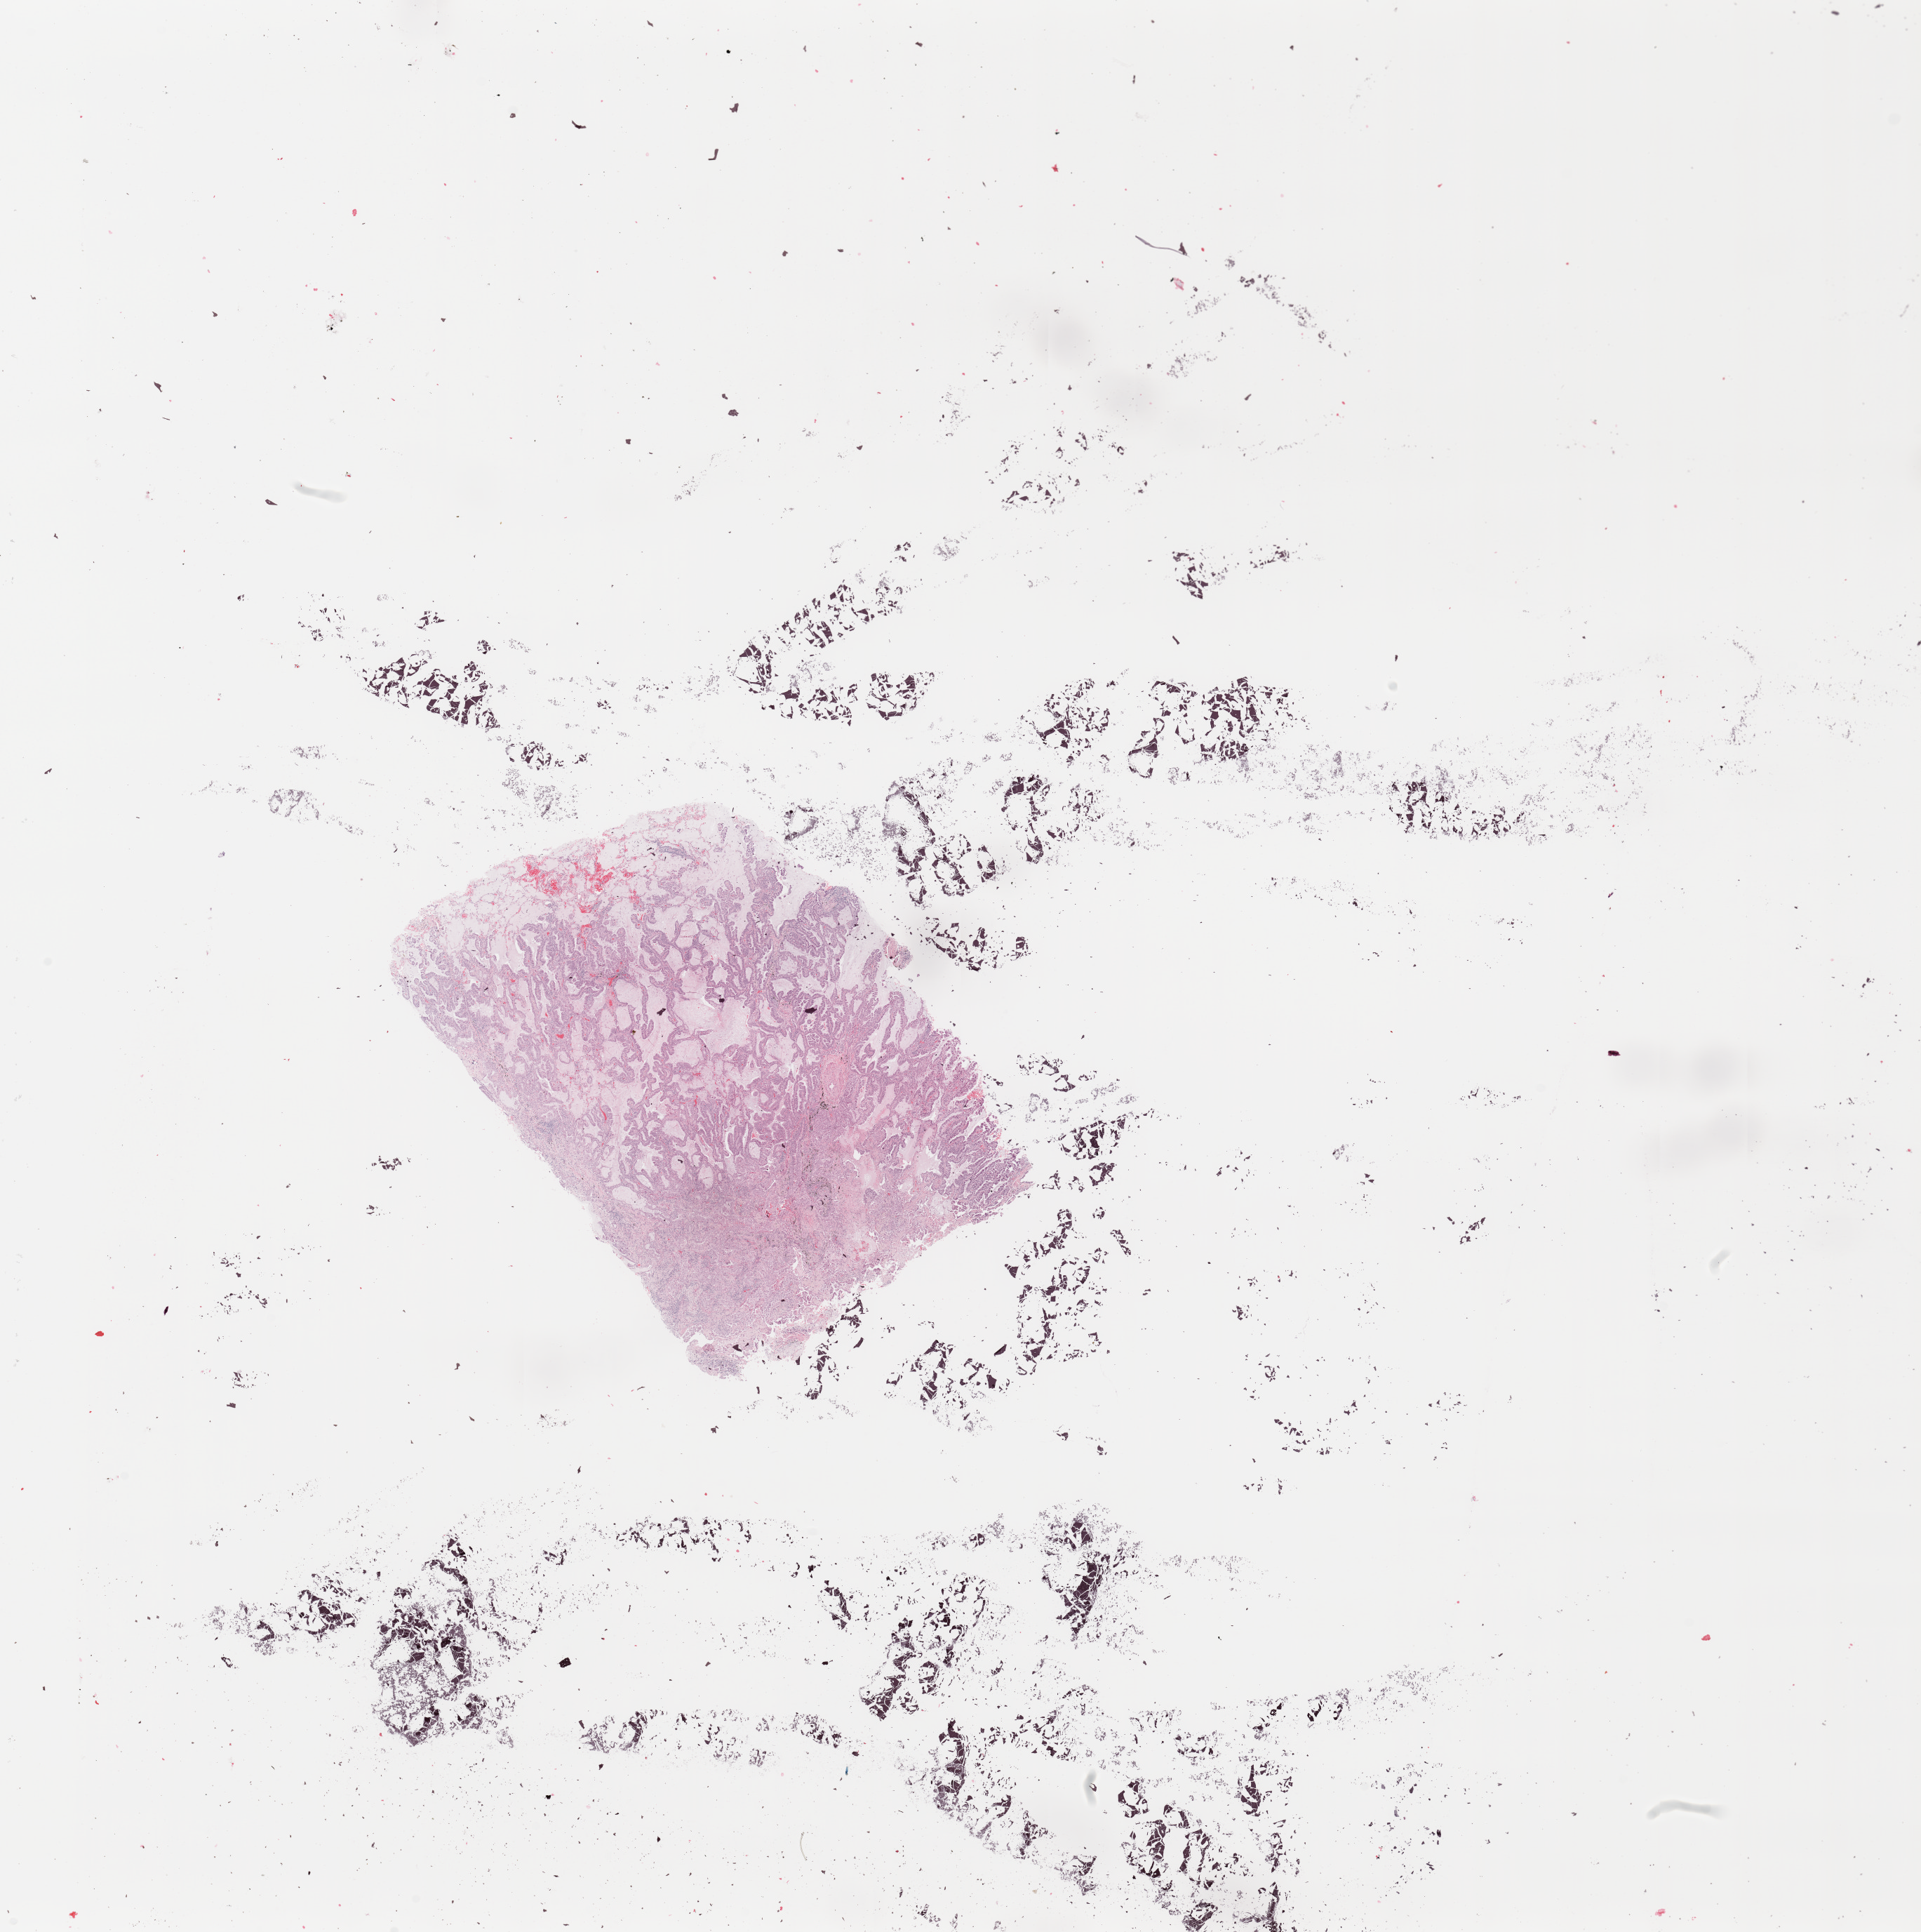
H&E whole-slide image — a low-resolution overview of the entire scanned area, about 21.7 x 21.8 mm, tumour tissue sample, sampled site: lung. Patient: male, age 64 years. Histologic grade: G3 (poorly differentiated). Composition of this section per pathologist review: tumour nuclei 75%, necrosis 5%.
Diagnosis: Adenocarcinoma, NOS. AJCC pathologic stage: IIB.